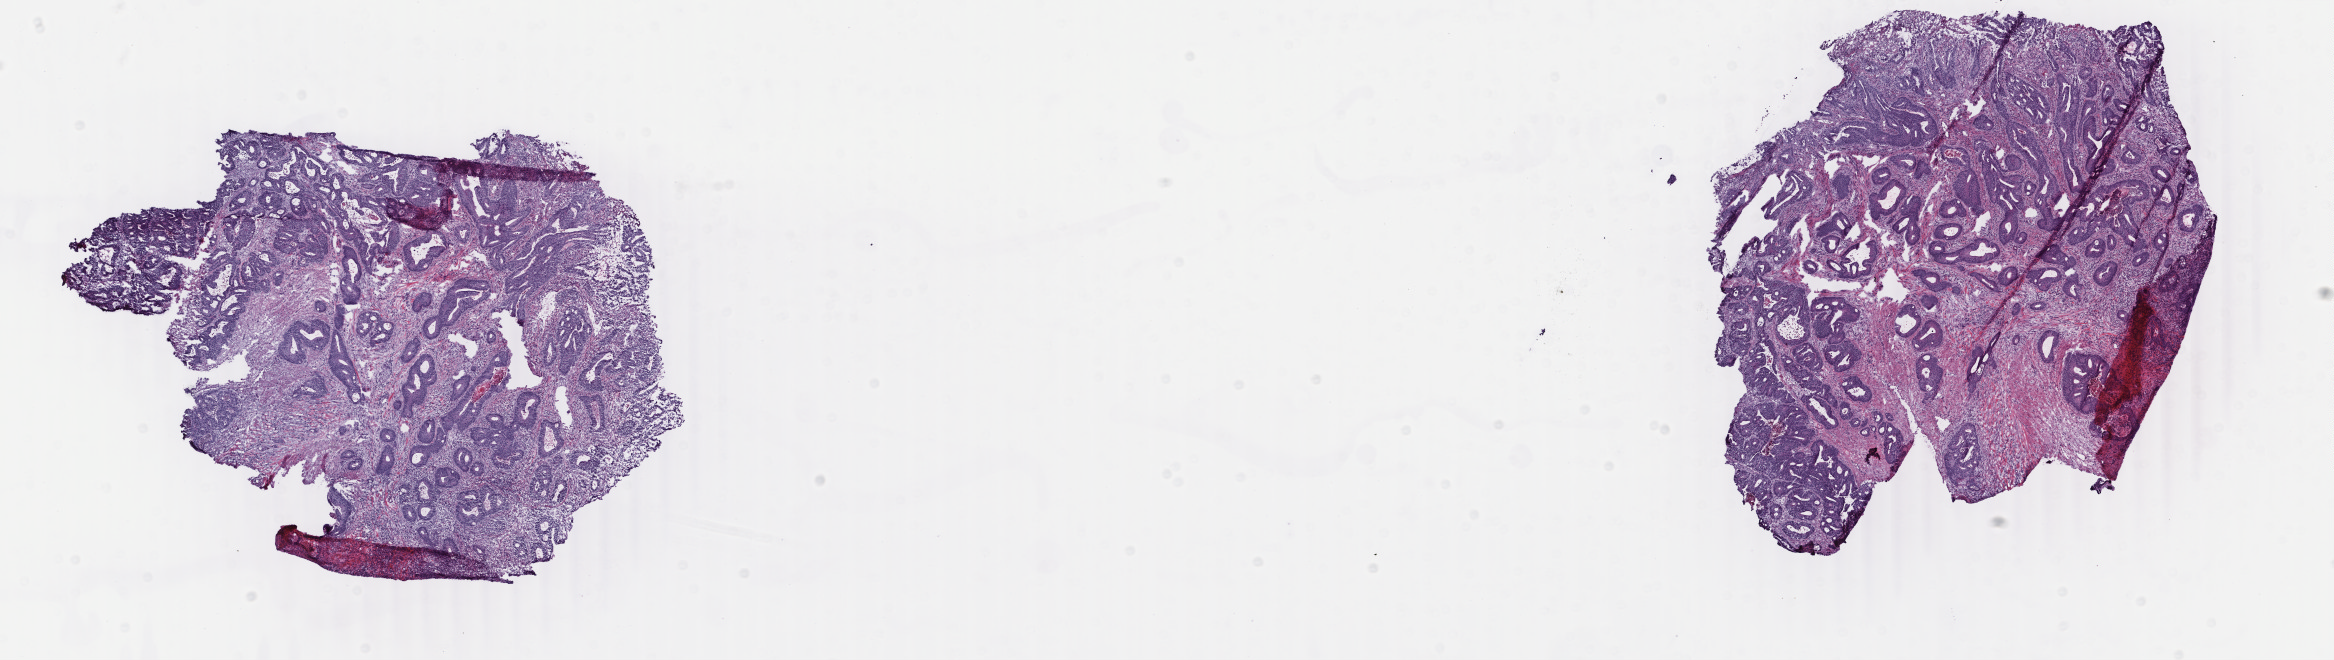
Digitized Hematoxylin and eosin (H&E) stained tissue section (whole slide) — shown as a low-resolution overview of the whole scanned area (about 18.6 x 5.2 mm), frozen section, colon, primary tumour sample. Female patient; age at initial diagnosis 57 years. Pathologist review of this section (percent, as recorded): tumour cells 80%, tumour nuclei 75%, normal cells 0%, stromal cells 15%, necrosis 5%. Infiltration values recorded for this section: lymphocyte infiltration 7%, monocyte infiltration 2%, neutrophil infiltration 7%.
• AJCC pathologic stage: IIA (6th edition)
• lymph nodes positive (case pathology): 0 of 18 examined
• diagnosis: Adenocarcinoma, NOS (sigmoid colon)